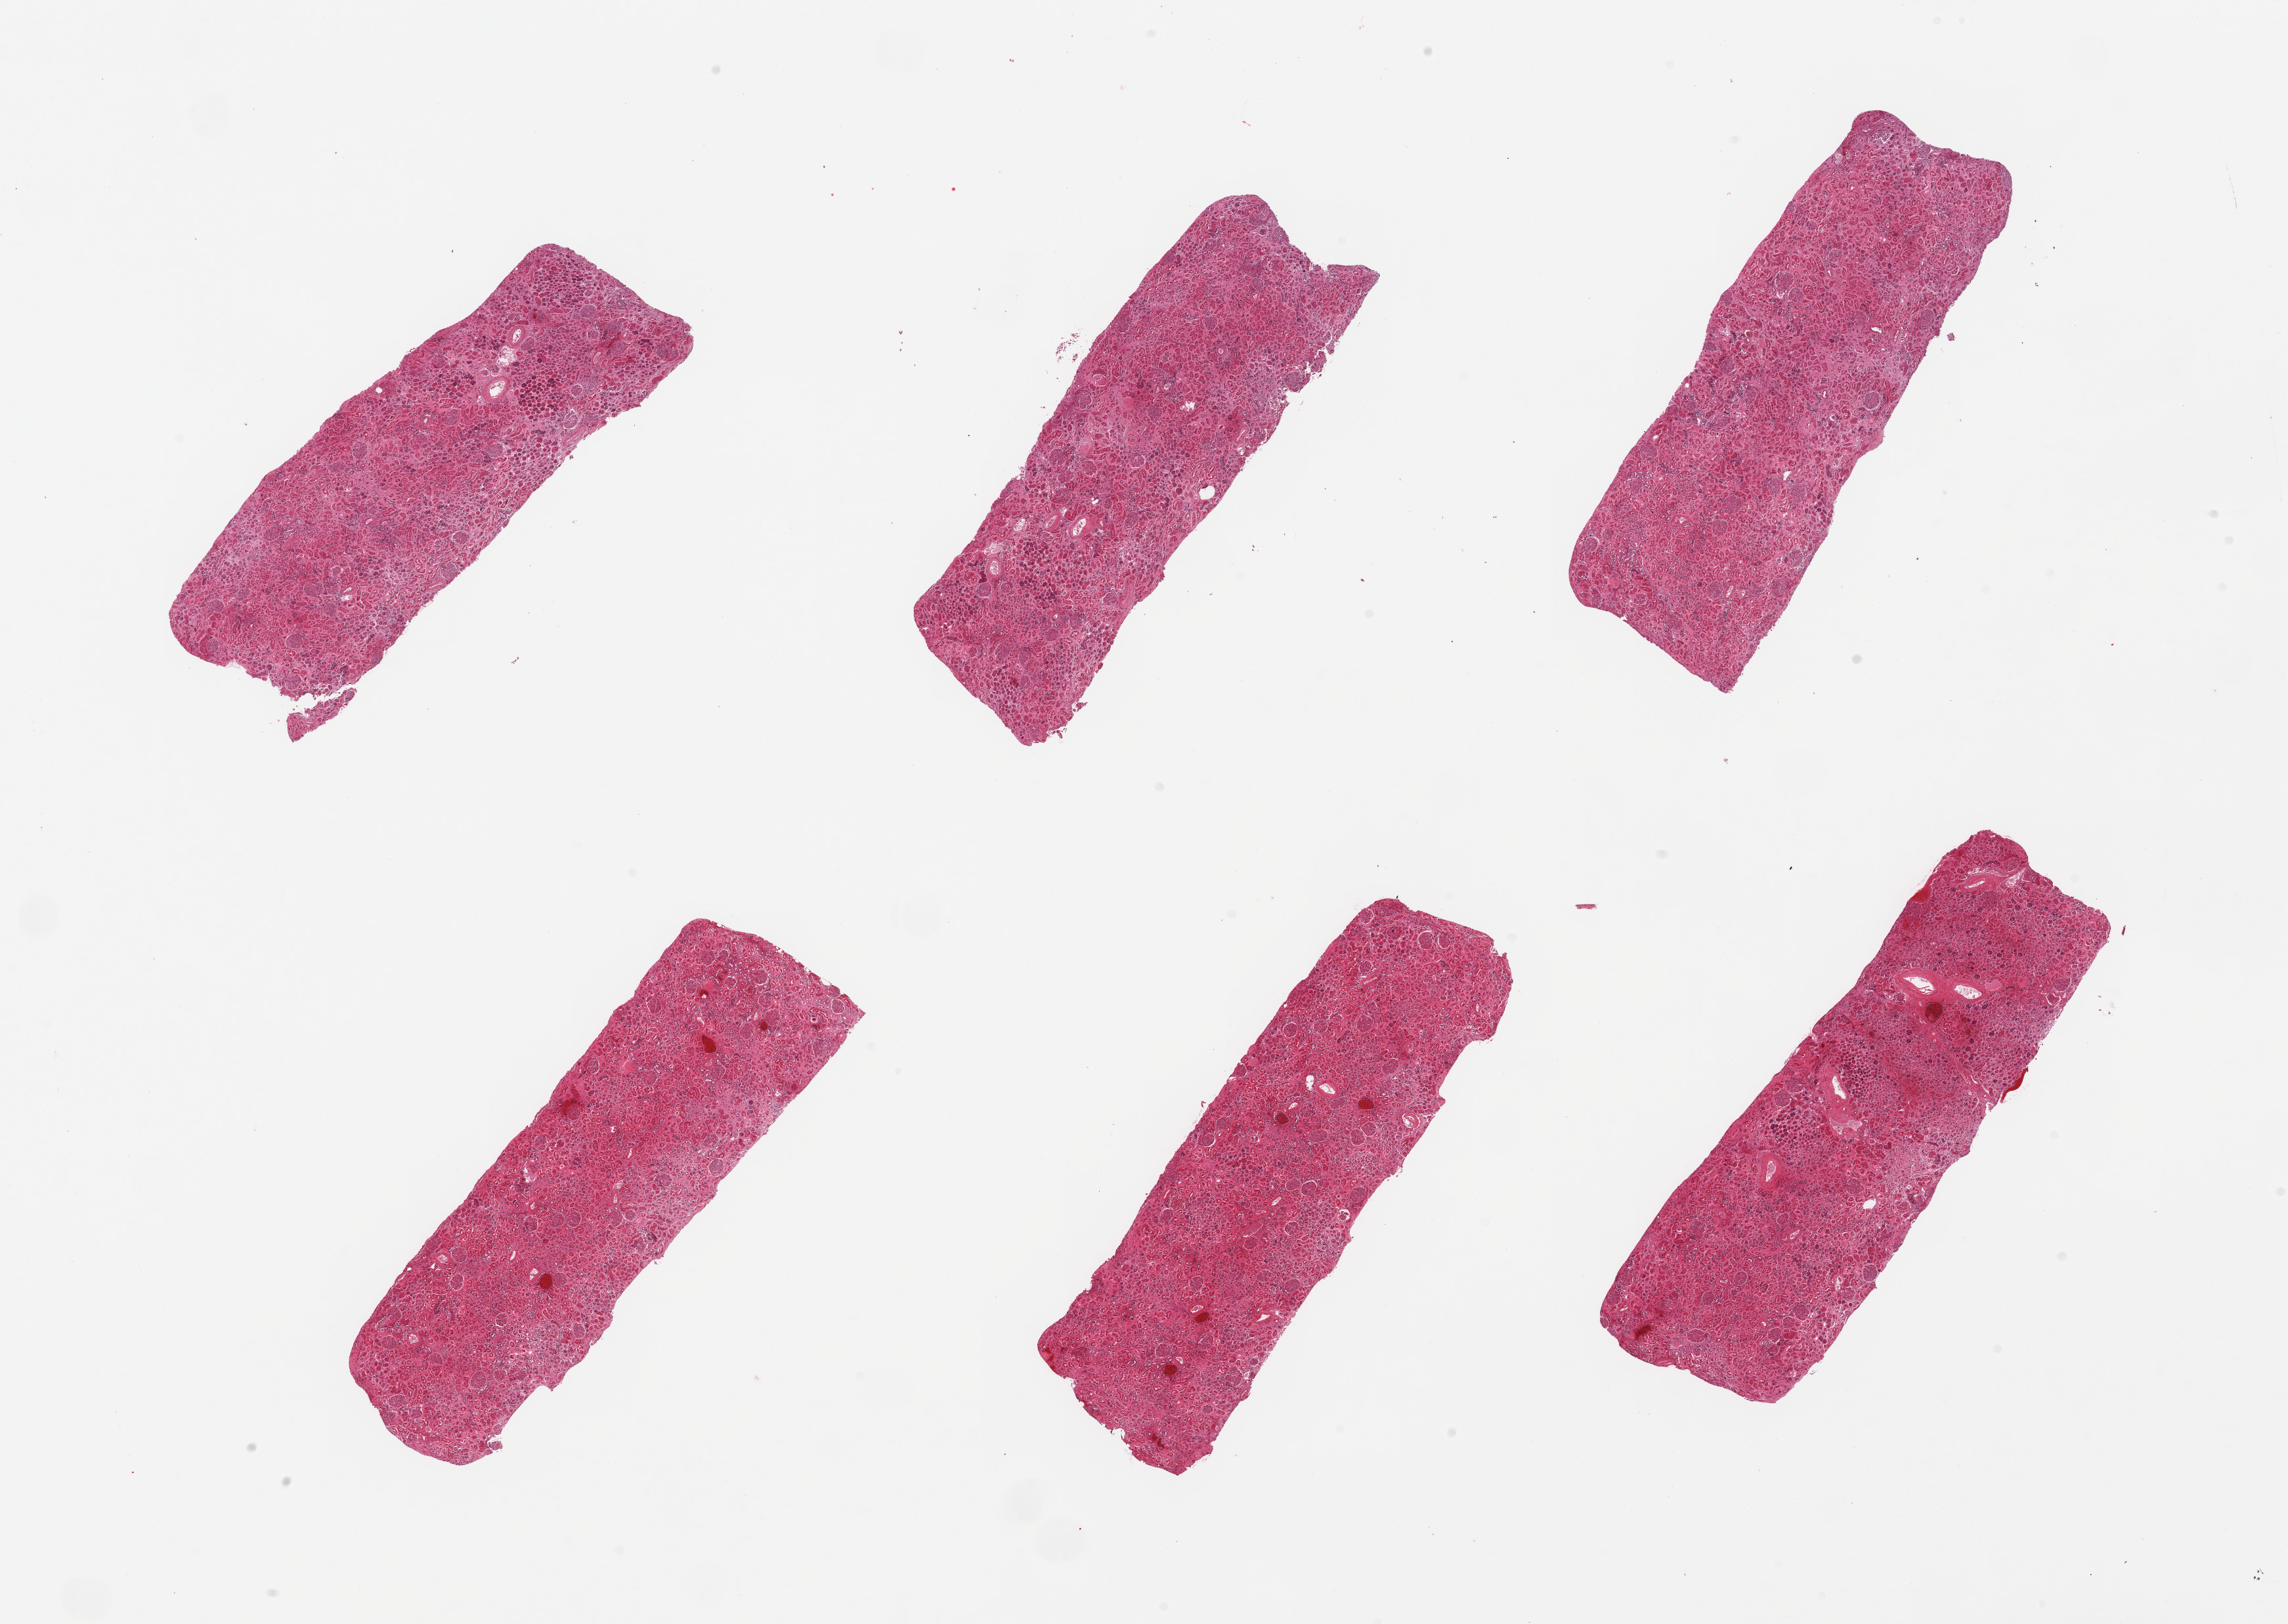
Whole-slide image, hematoxylin and eosin (H&E) stain, brightfield, low-resolution overview of the scanned area, about 27.6 x 19.6 mm (acquisition: 20x scan); PAXgene-fixed, paraffin-embedded tissue; target tissue: renal cortex; tissue donor sample. Male donor.
* pathologist's review note for this sample: 6 pieces; arterial & arteriolosclerosis and scattered sclerosed glomeruli